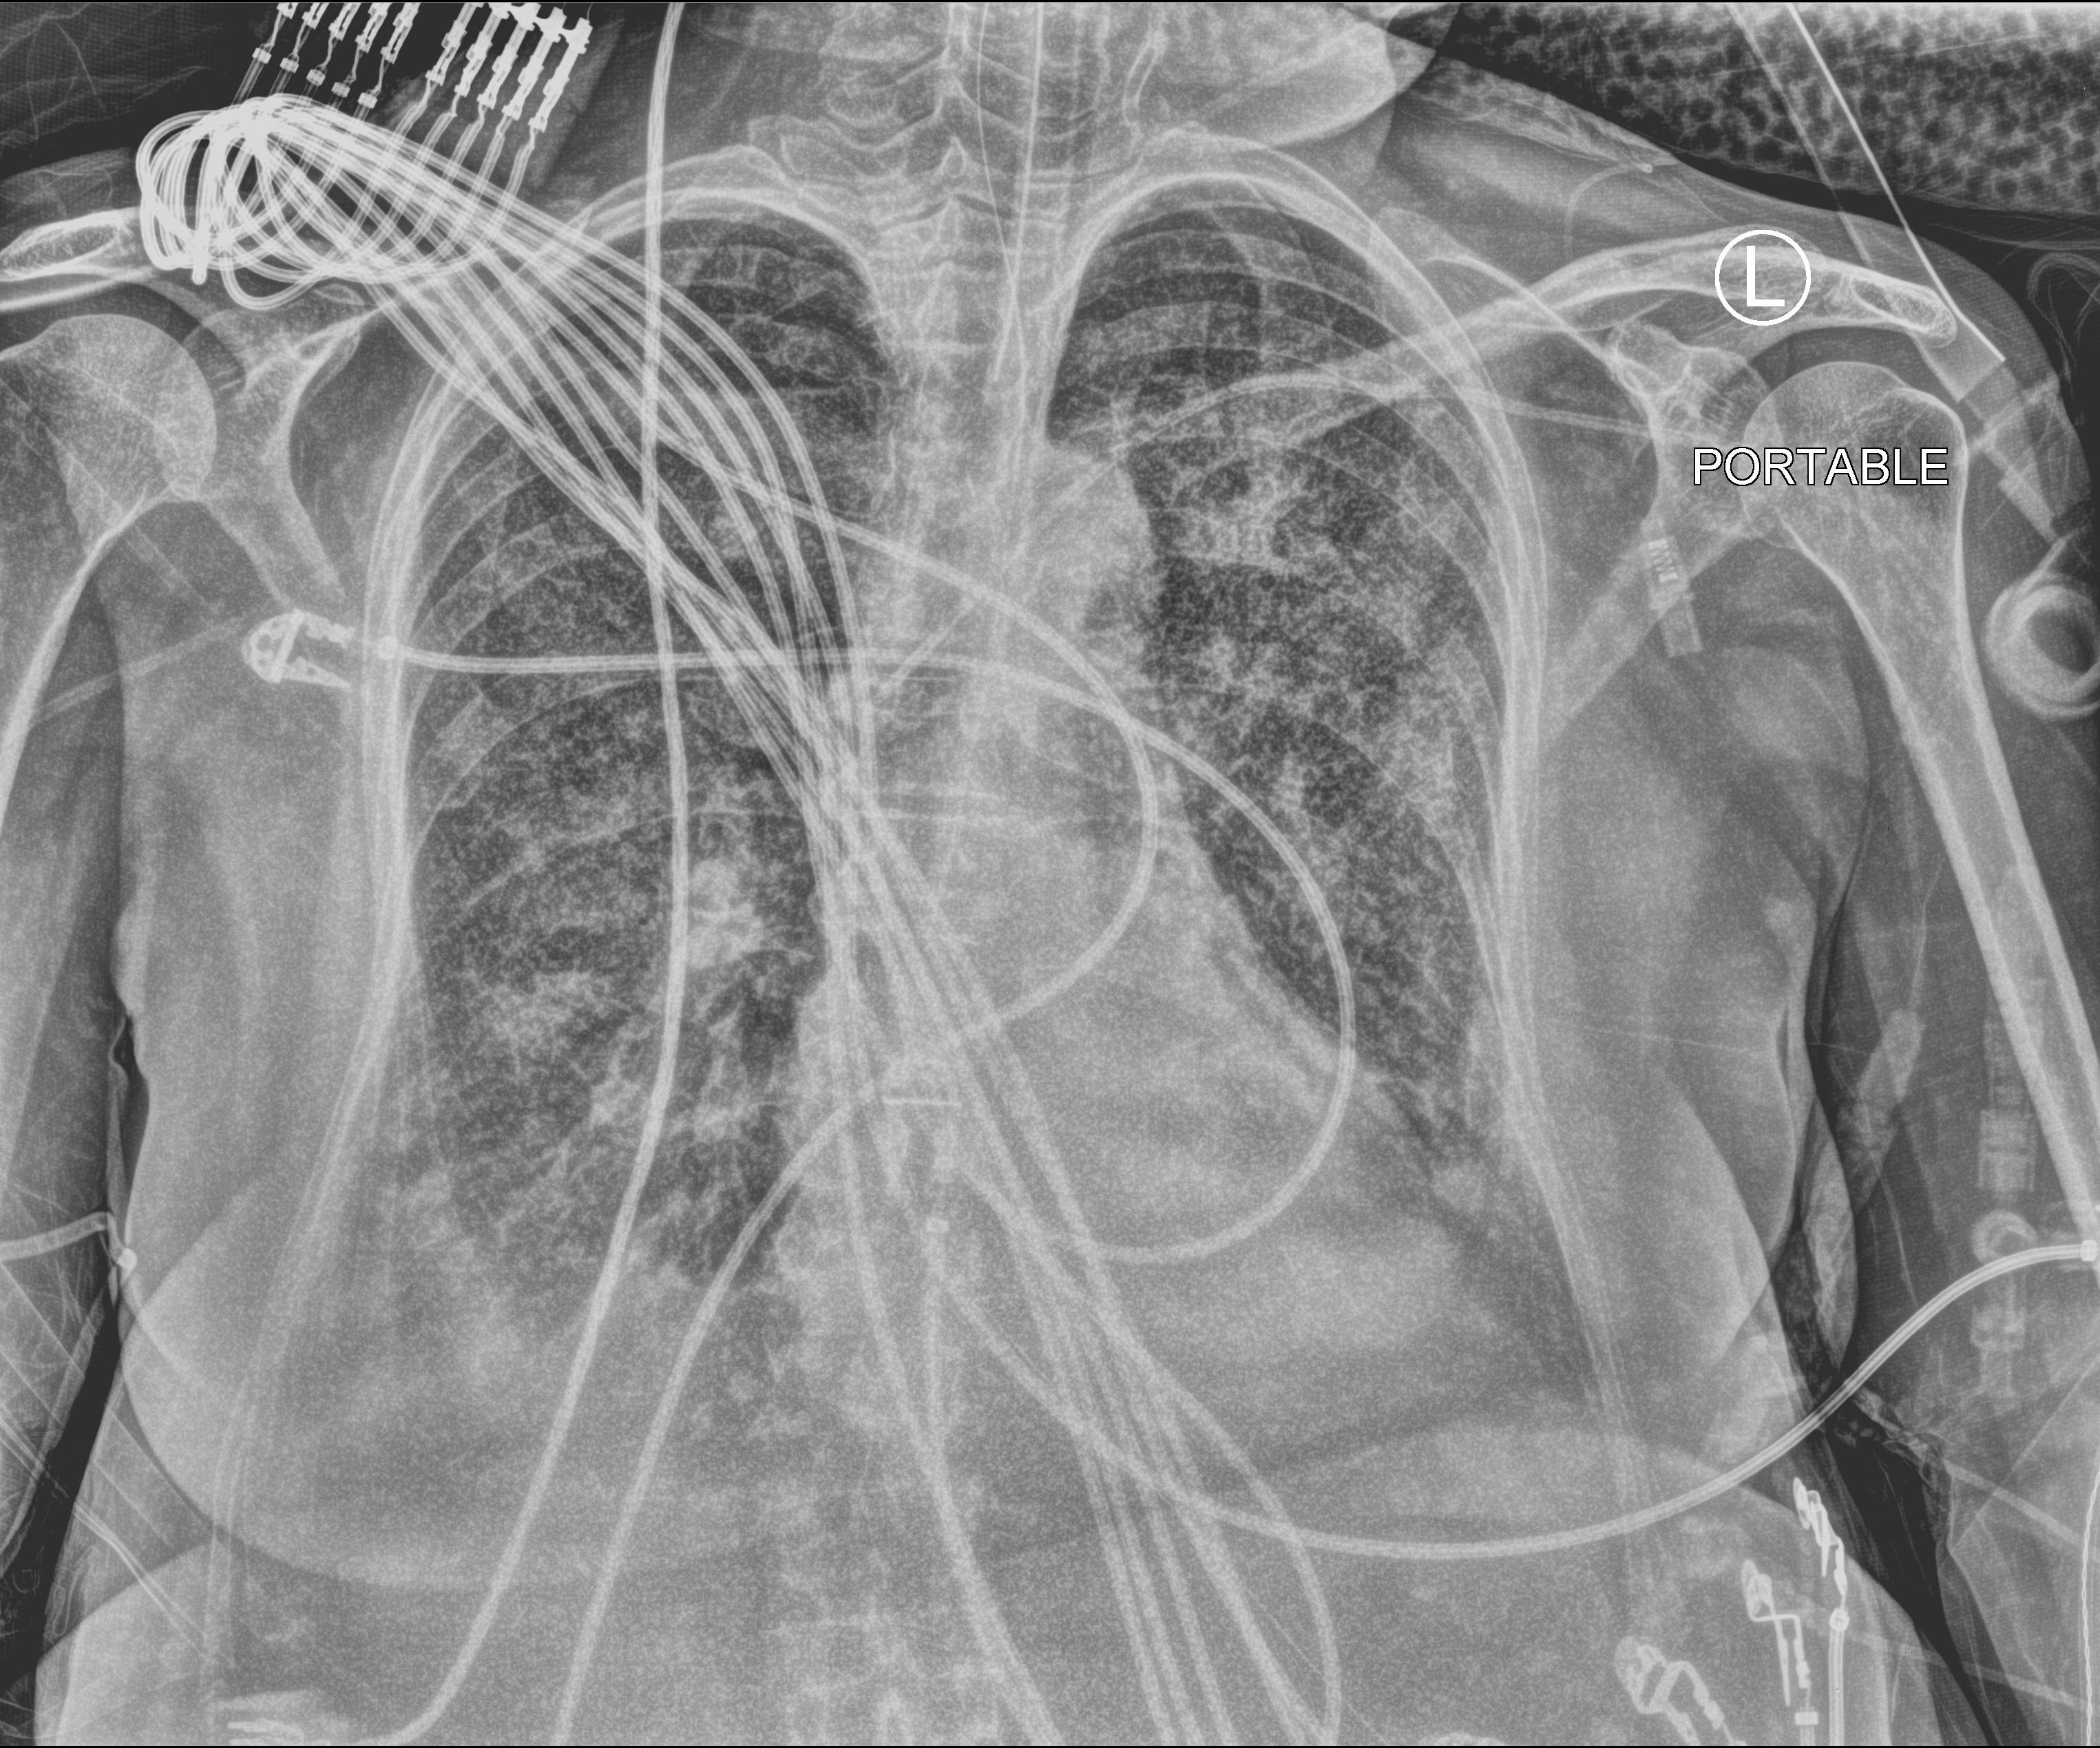
Portable chest radiograph, anteroposterior (AP) projection. Female patient hospitalised with COVID-19, age 75–90 years.
Hospital-stay facts (about this admission, not read from this image; timing relative to this image not recorded): diabetes (admission record): no; length of hospital stay: 70 days; admitted to intensive care during this hospital stay: yes.